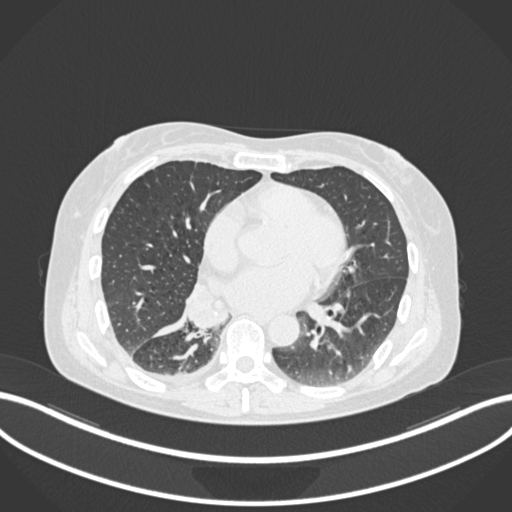
Chest CT, one axial slice. Position 70 of 168 along the scan axis. 120 kVp. Lung window (W 1500 / L -600 HU). 512 × 512 image matrix, field of view 400 × 400 mm. Patient: female, 63 years. From the clinical record (not read from this slice): clinical TNM (as recorded): T1c N0 M0.
Annotated regions visible in this slice (bounding box drawn by a radiologist):
- lung tumour (recorded histology: adenocarcinoma): bounding box <176,273,235,337> (left, top, right, bottom; pixels)